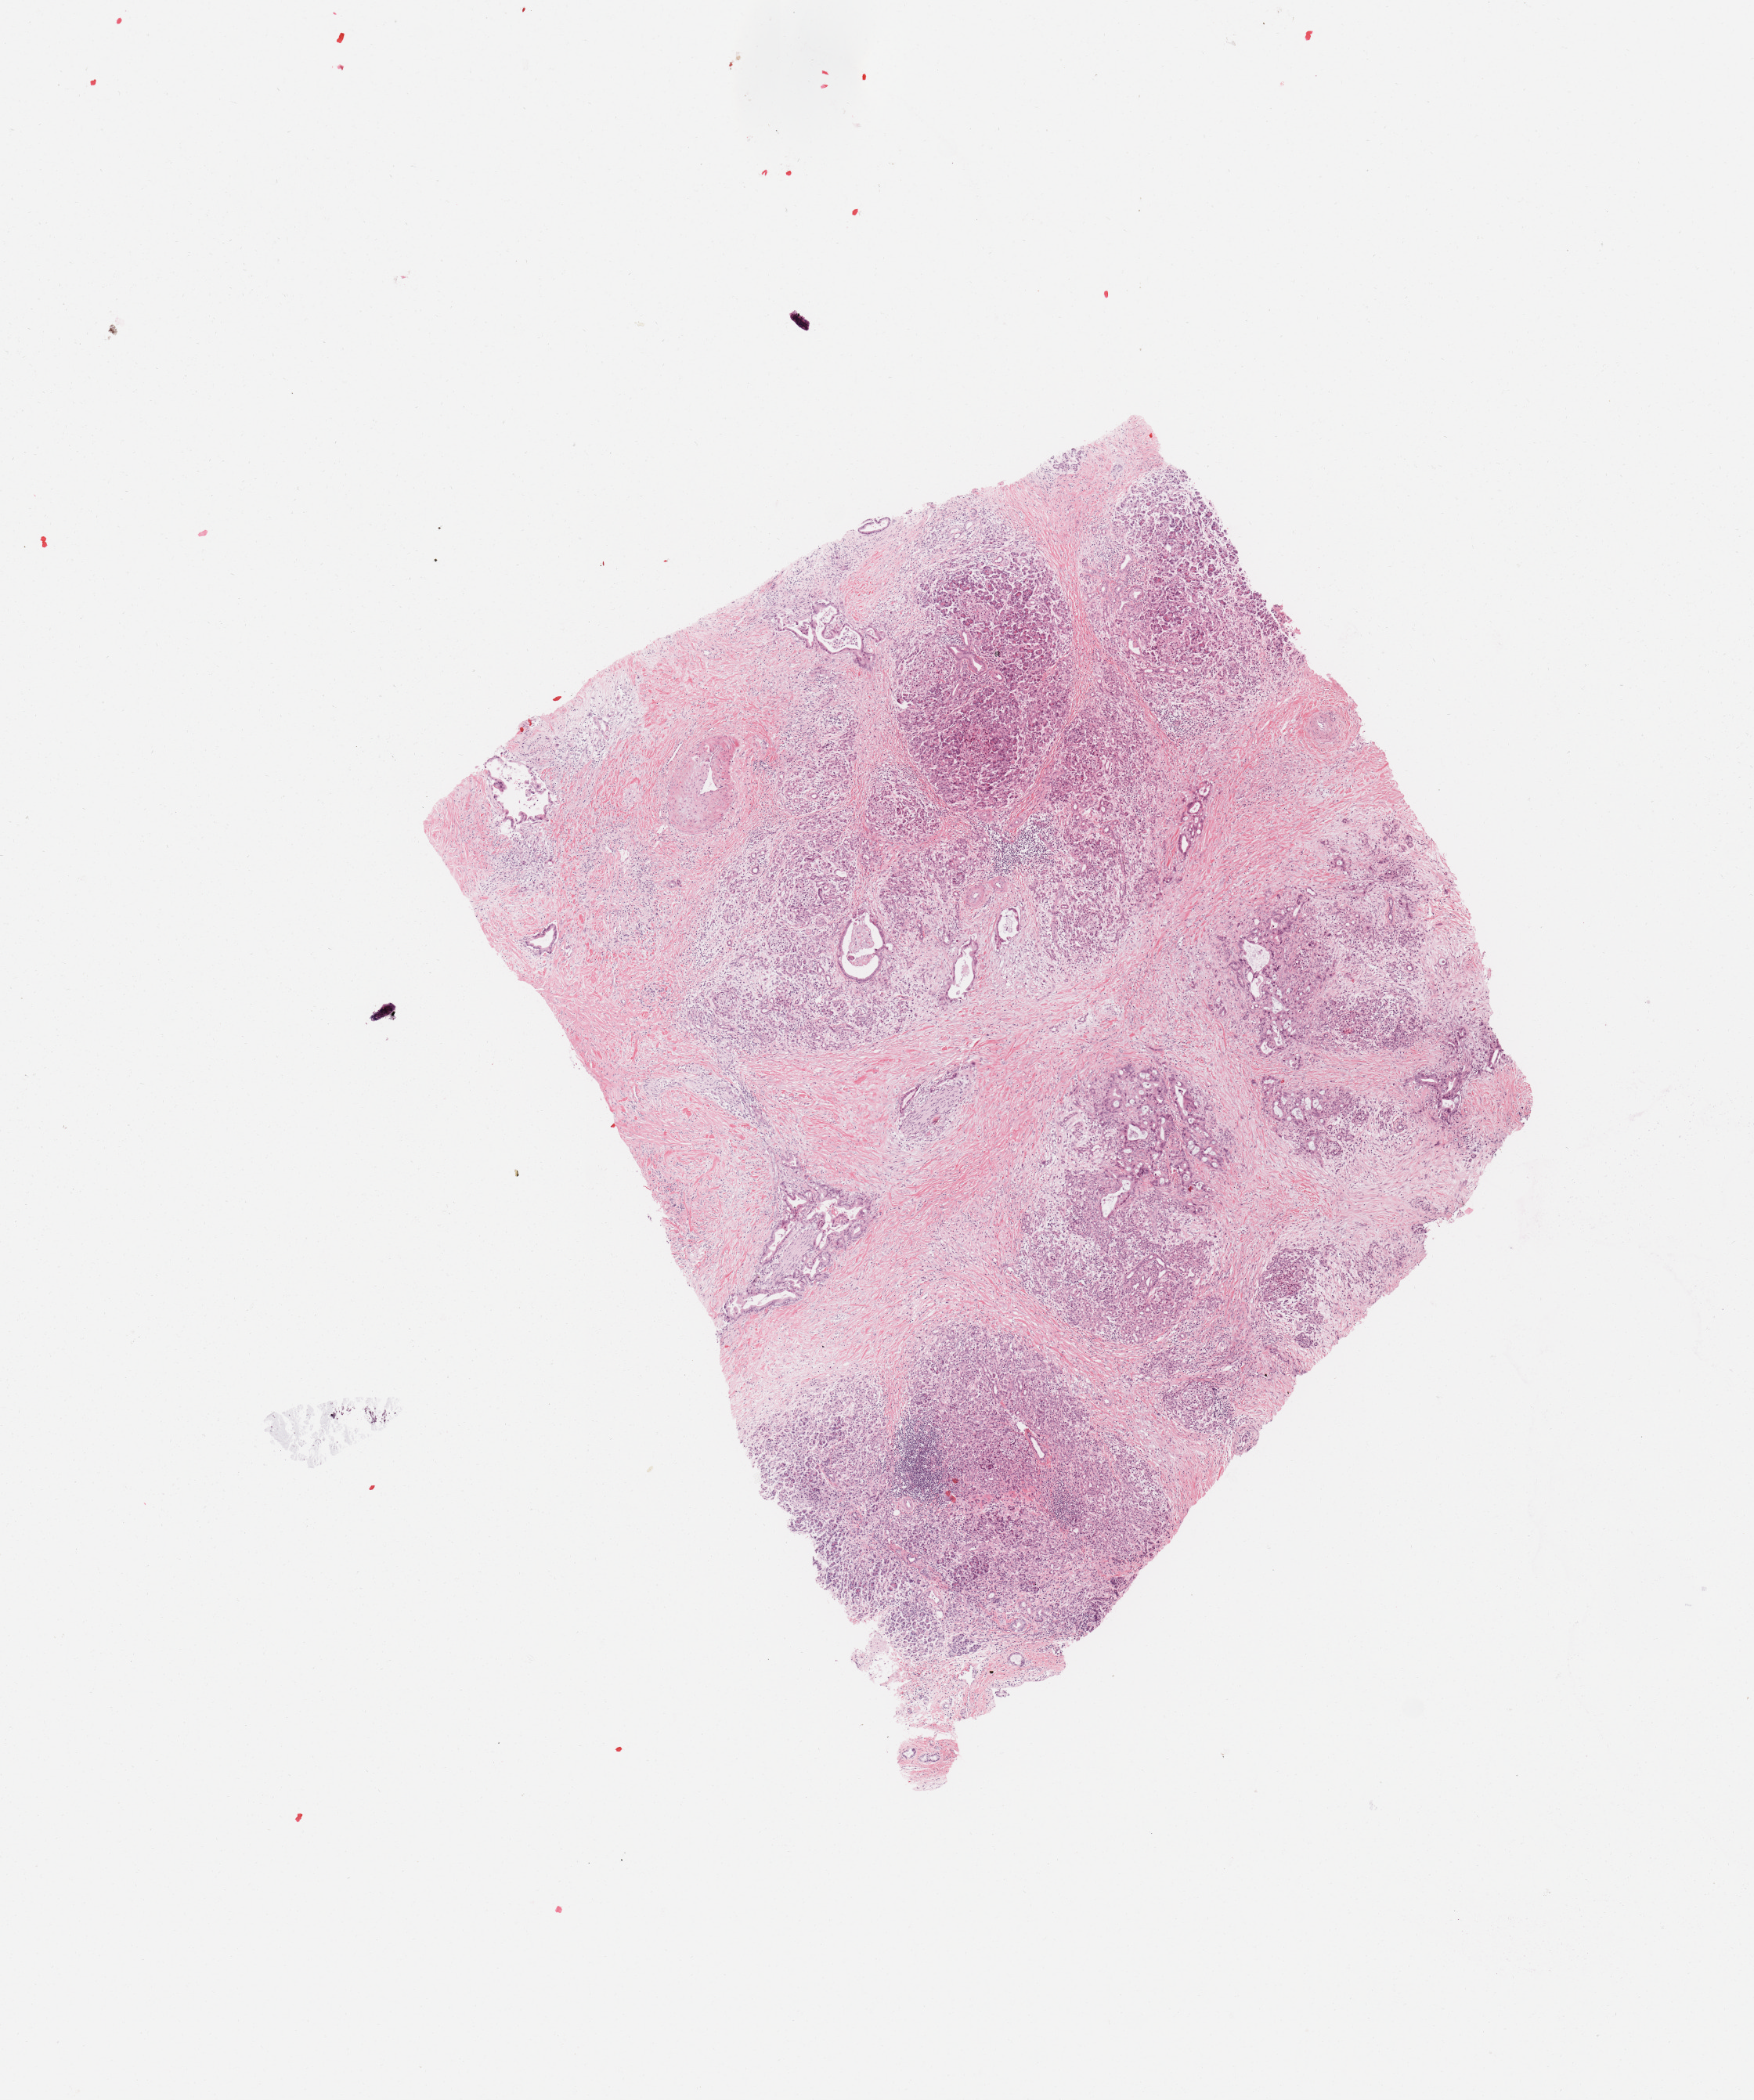
Digitized H&E-stained tissue section (whole slide) — whole scanned area (about 8.9 x 10.6 mm, from a 20x scan) shown as a low-resolution overview. Tumour tissue sample, sampled site: pancreas. 59-year-old female patient. Histologic grade: G2 (moderately differentiated). Pathologist review of this section (percent, as recorded): tumour nuclei 10%, necrosis 0%.
Primary tumour site (as recorded): body. AJCC pathologic stage: IIB. Histologic diagnosis: Infiltrating duct carcinoma, NOS.